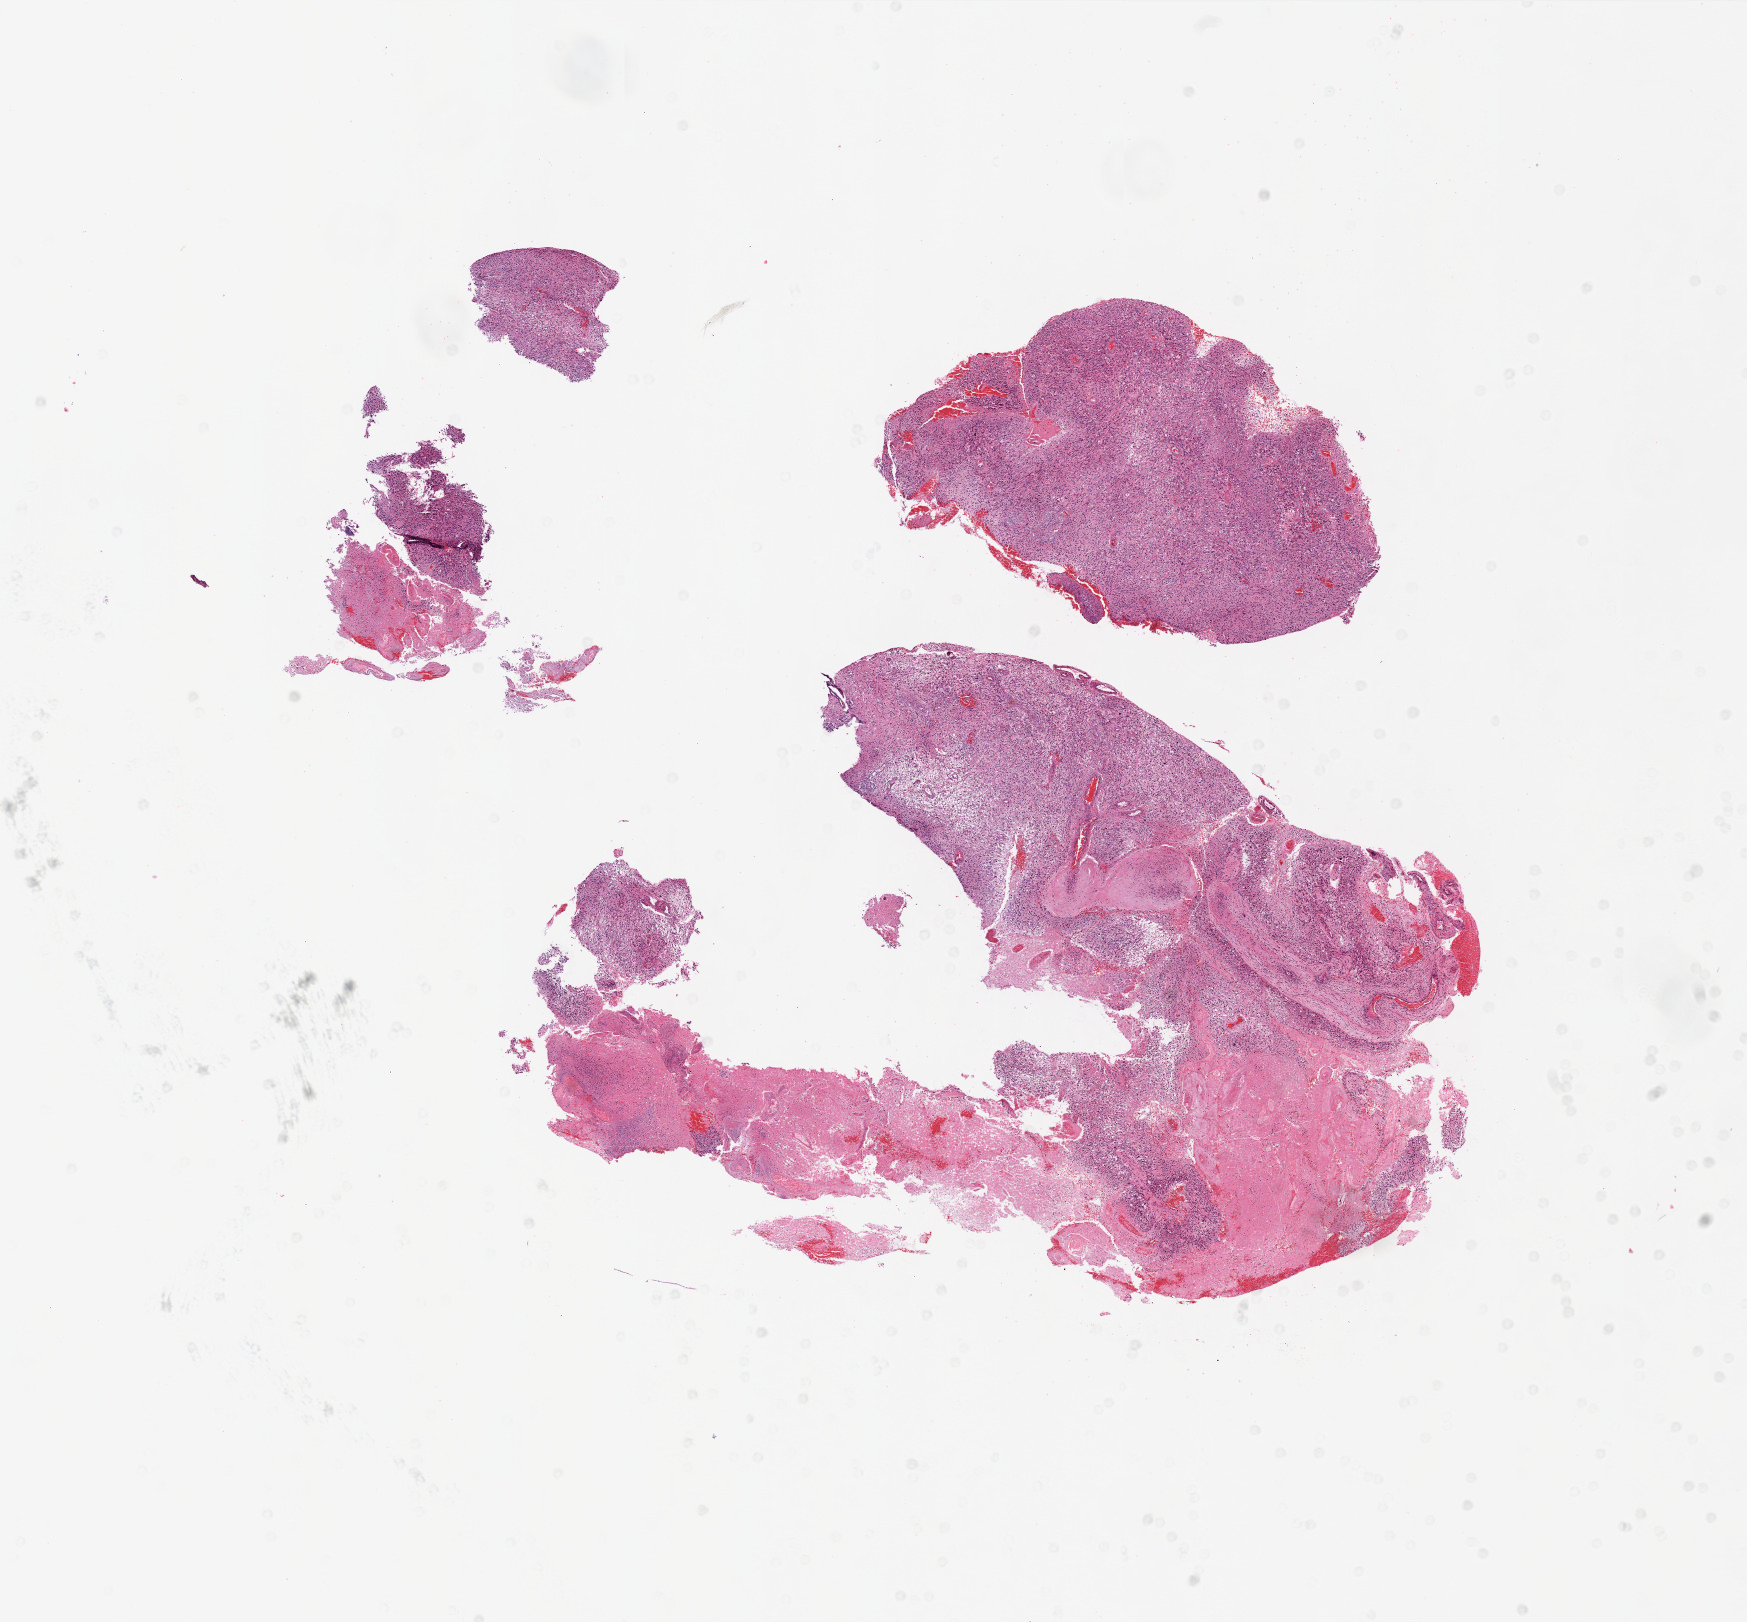
H&E whole-slide image, a low-resolution overview of the entire scanned area, about 14.0 x 13.0 mm, FFPE section, primary tumour sample from the brain. Female patient; age at initial diagnosis 72 years.
Pathologic diagnosis: Glioblastoma.